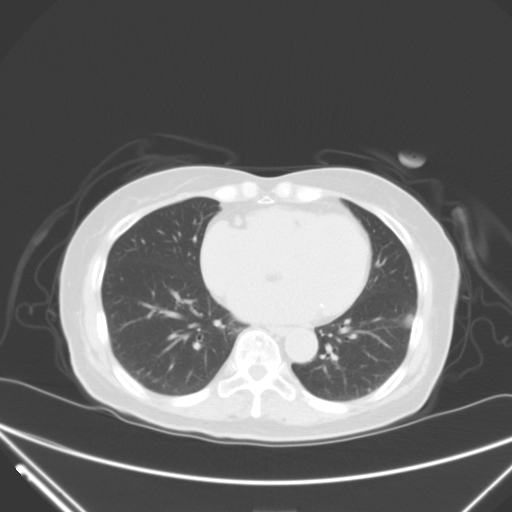
Chest CT, one axial slice; slice 24 of 62 in the series (ordered by position); 120 kVp; lung window (W 1500 / L -600 HU); 5 mm slice thickness; 512 × 512 image matrix. Female patient, age 82 years. Case-level facts recorded for this patient, not image findings: clinical TNM (as recorded): T1c N0 M0.
Annotated regions visible in this slice (rectangle marked by the reading radiologist):
- lung tumour (recorded histology: adenocarcinoma): bounding box <398,306,419,338> (left, top, right, bottom; pixels)